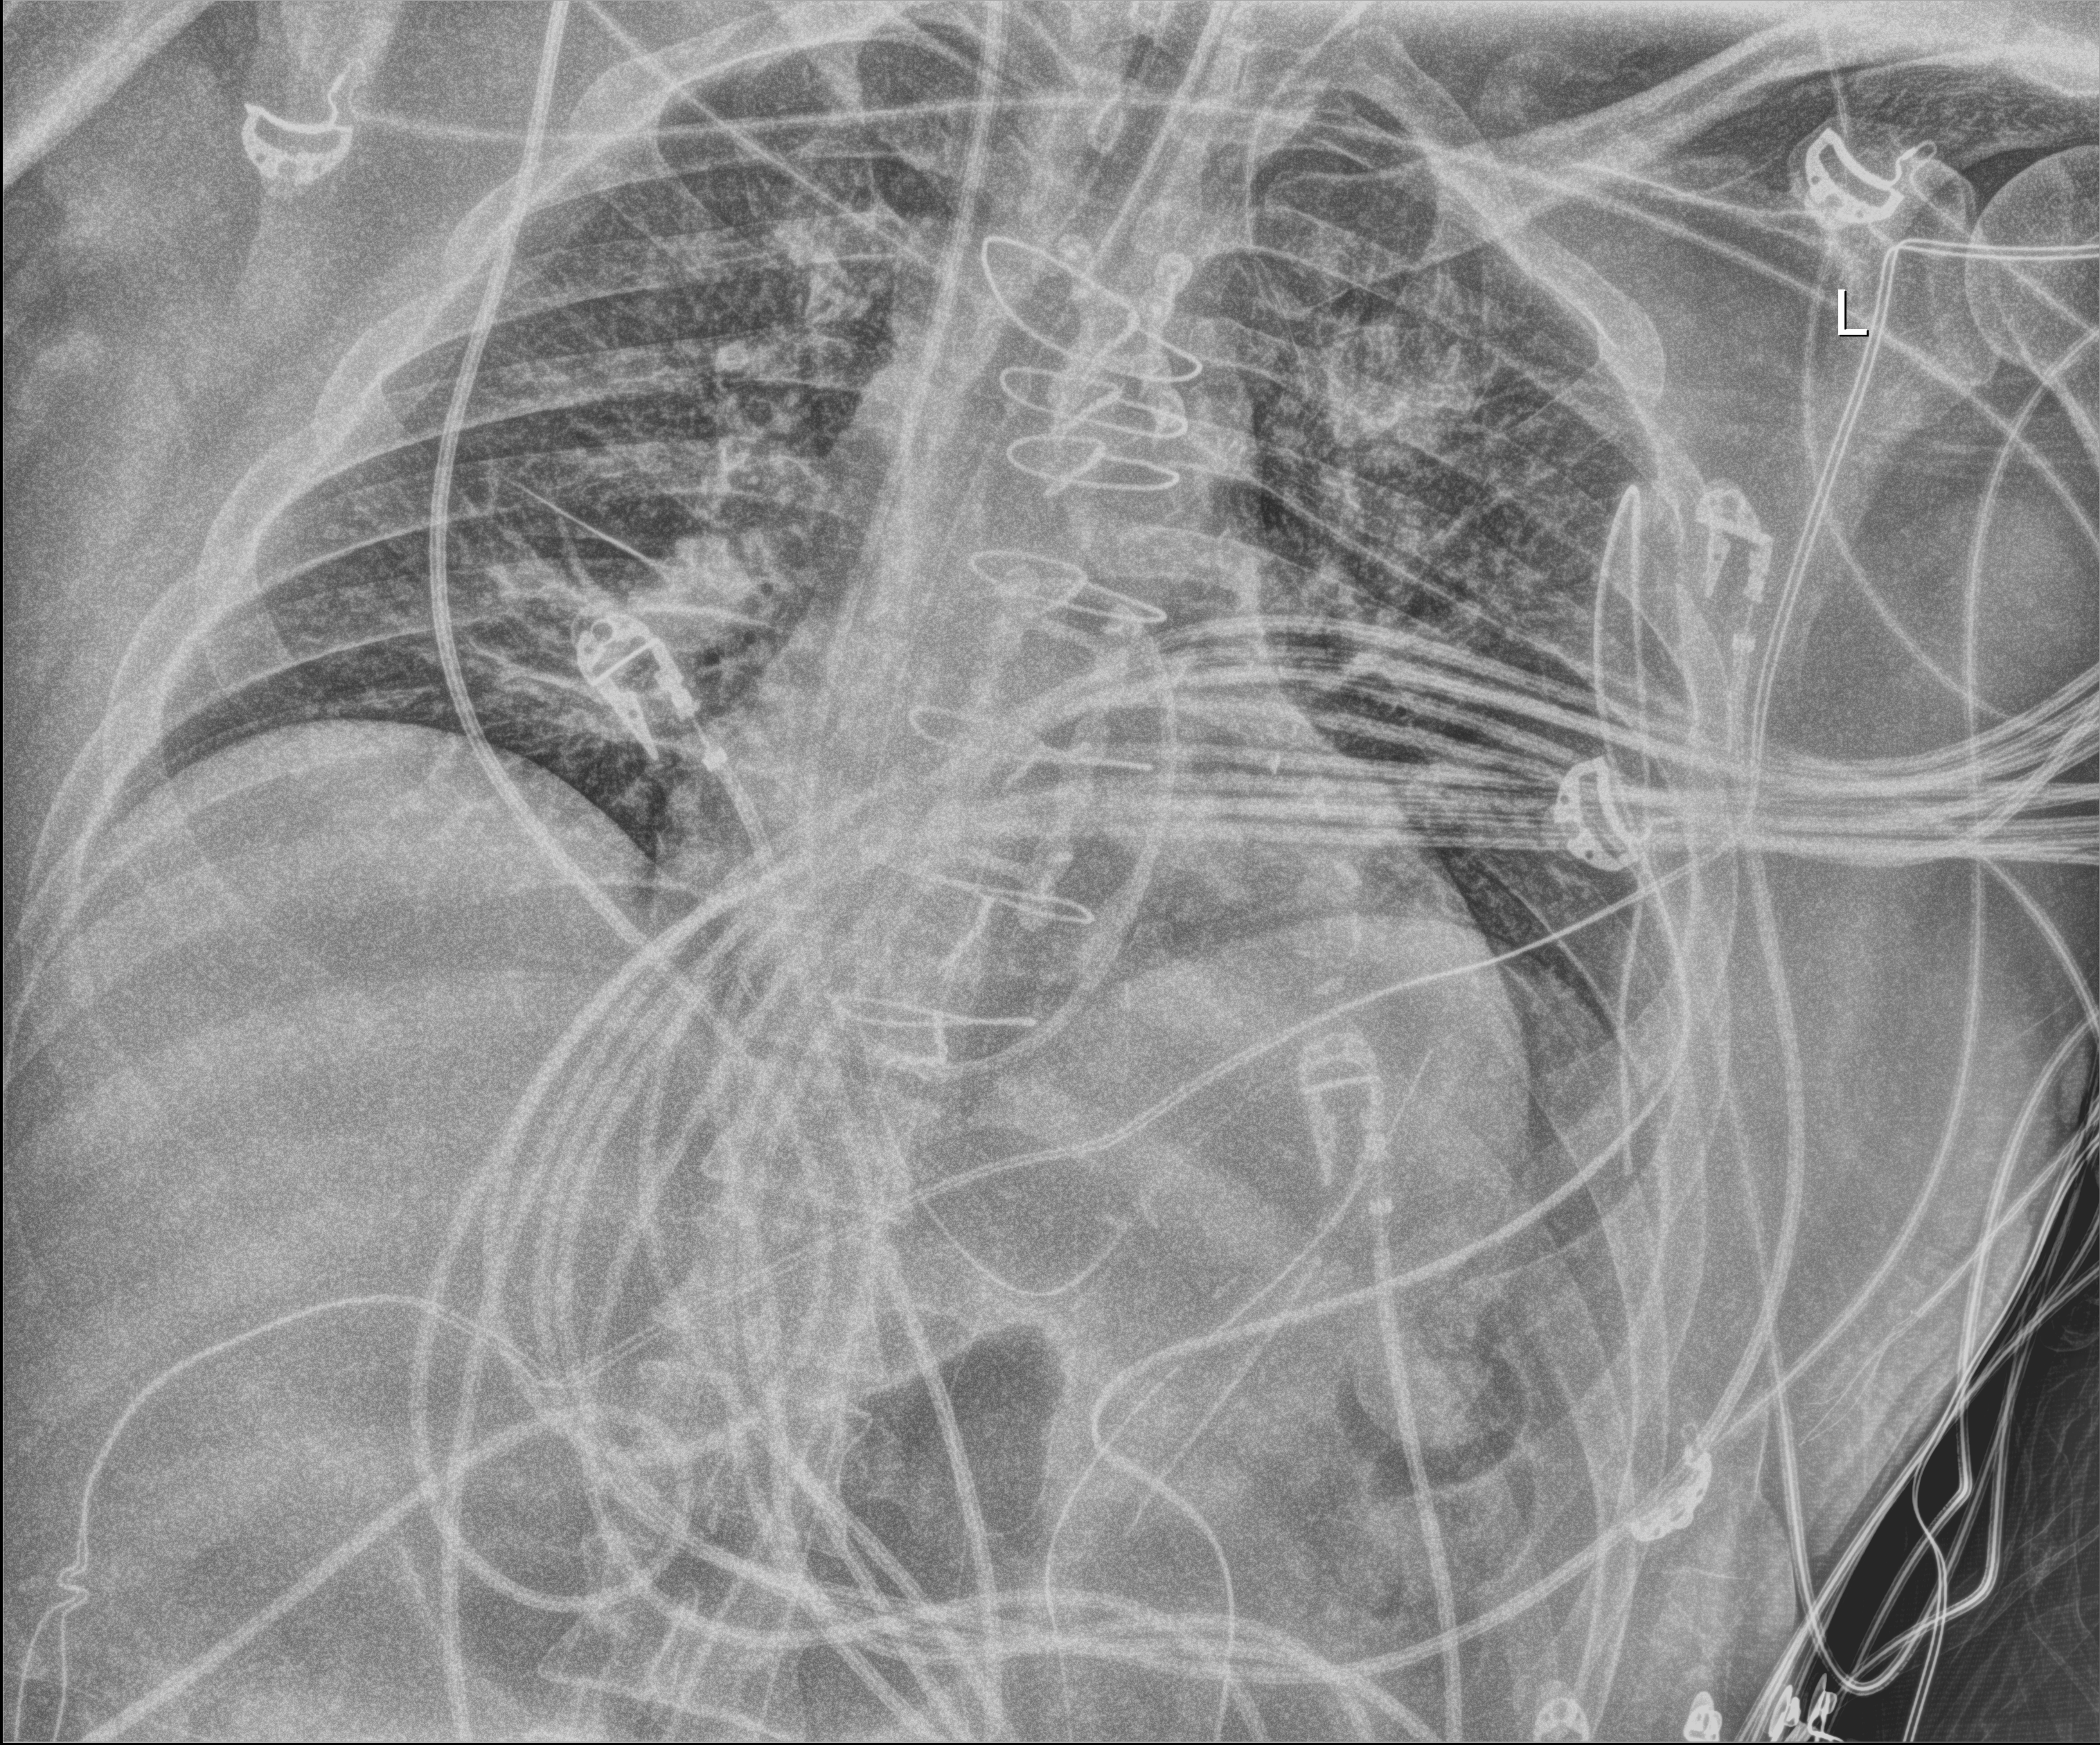
Chest X-ray (portable), anteroposterior (AP) projection. Patient hospitalised with COVID-19; male, aged 18–59 years.
From the hospital-stay record, not from the radiograph (when in the stay this image was taken is not recorded):
- length of hospital stay: 17 days
- admitted to intensive care during this hospital stay: no